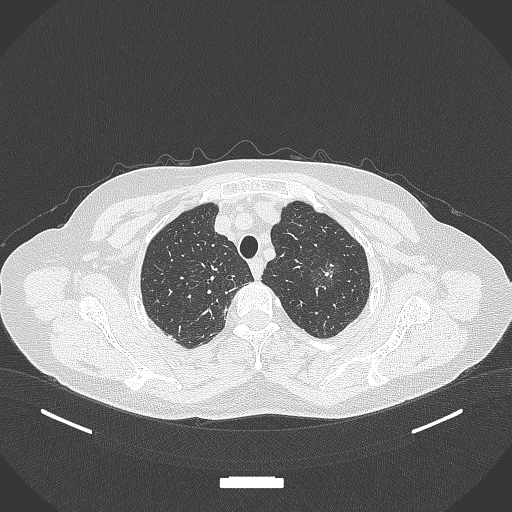
Chest CT, one axial slice. Slice 303 of 369 in the series (ordered by position). Reconstruction kernel B70f. Lung window (W 1500 / L -600 HU). 1 mm slice thickness. 512 × 512 image matrix, field of view 400 × 400 mm. Patient: female, 64 years. Case-level facts recorded for this patient, not image findings: clinical TNM (as recorded): T1c N0 M0; histopathological grade: G1.
Annotated regions visible in this slice (rectangle marked by the reading radiologist):
- lung tumour (recorded histology: adenocarcinoma): bounding box (x1, y1, x2, y2) in pixels: (307, 253, 344, 297)